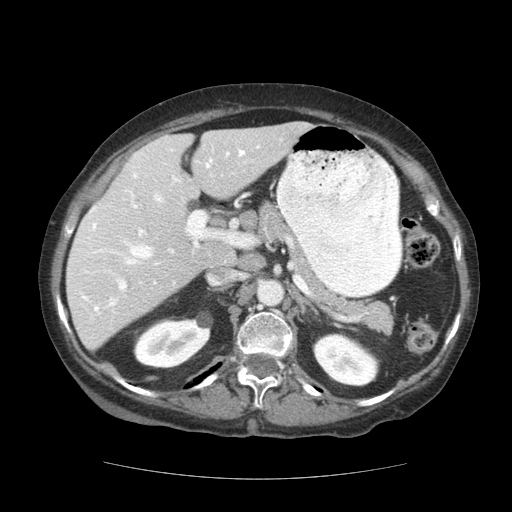
Contrast-enhanced abdominal CT (liver protocol), one axial slice; position 72 of 111 along the scan axis; 140 kVp; soft-tissue window (W 400 / L 40 HU); 512 × 512 image matrix, field of view 360 × 360 mm. Case-level facts recorded for this patient, not image findings: diagnosis: hepatocellular carcinoma (patient treated with transarterial chemoembolisation; whether this scan precedes or follows treatment is not stated here); TNM stage (as recorded): Stage-I; Child-Pugh class: A; tumour differentiation: moderately-poorly differentiated; tumour nodularity: uninodular.
Outlined on this slice (semi-automatically segmented with operator editing):
- liver parenchyma outside the tumour (the mass and vessels are separate outlines, so this box may not span the whole liver): box from (x=66, y=122) to (x=310, y=350) px
- liver vessels: (x=80, y=145)–(x=260, y=314)